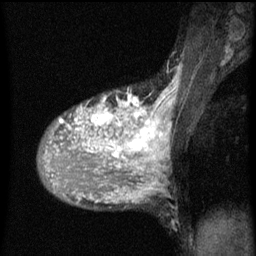
Breast MRI (dynamic contrast-enhanced), one sagittal slice; position 35 of 60 along the scan axis; dynamic contrast-enhanced series, image 2 of 3 at this slice position (ordered by acquisition); 1.5 T; TE 4.2 ms, TR 8 ms; 2 mm slice thickness; 256 × 256 image matrix. Patient: female, 36 years.
Annotated regions visible in this slice (semi-automatically segmented with operator editing):
- analysis volume of interest (the breast-tissue region the enhancement analysis was run in; not a lesion): box from (x=40, y=92) to (x=167, y=161) px
- tumour enhancement mask (voxels above the 70 % enhancement threshold inside the analysis volume of interest): (x=44, y=94)–(x=167, y=161)